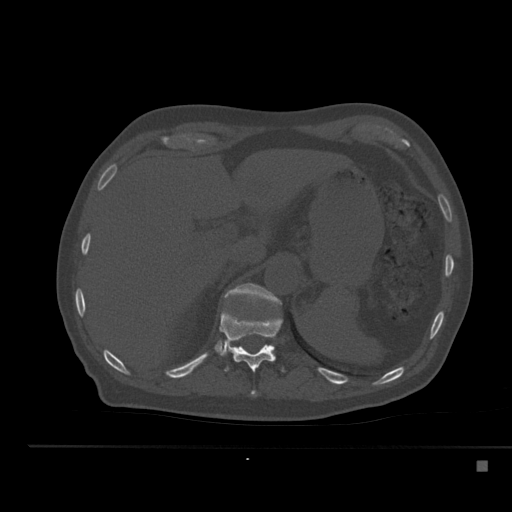
CT including the spine, one axial slice; position 246 of 517 along the scan axis; reconstruction kernel Br40s; 120 kVp; bone window (W 1800 / L 400 HU); 1.5 mm slice thickness; 512 × 512 image matrix. Male patient, age 70 years. From the clinical record (not read from this slice): primary cancer: renal; vertebrae with lytic lesions (as recorded): T4, T6, T10, T12, L3, L4, L5.
Annotated regions visible in this slice (semi-automatic segmentation, software-assisted and operator-edited):
- T11 vertebra: box from (x=219, y=310) to (x=284, y=397) px
- T12 vertebra: (x=224, y=283)–(x=281, y=359)